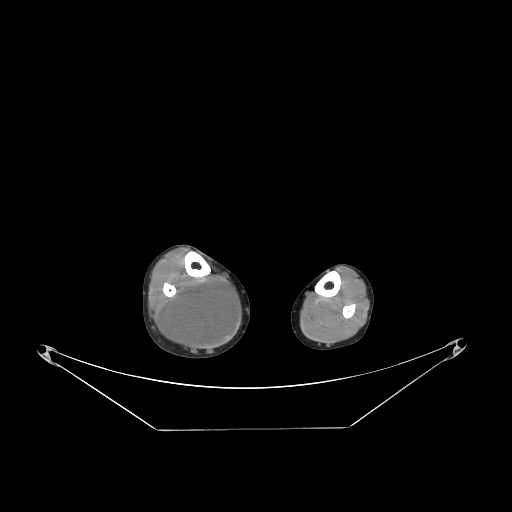
CT of an extremity soft-tissue mass (from a PET/CT study), one axial slice. Position 82 of 267 along the scan axis. Reconstruction kernel STANDARD. Soft-tissue window (W 400 / L 40 HU). 3.75 mm slice thickness. 512 × 512 image matrix, field of view 500 × 500 mm. Male patient. Case-level facts recorded for this patient, not image findings: histological type: liposarcoma - round cell; grade: high; site of the primary tumour: right calf.
Structures marked on this image (expert contour drawn on MRI and transferred to this co-registered scan by the dataset authors):
- gross tumour volume (mass): bounding box [x1, y1, x2, y2] px = [164, 276, 239, 346]